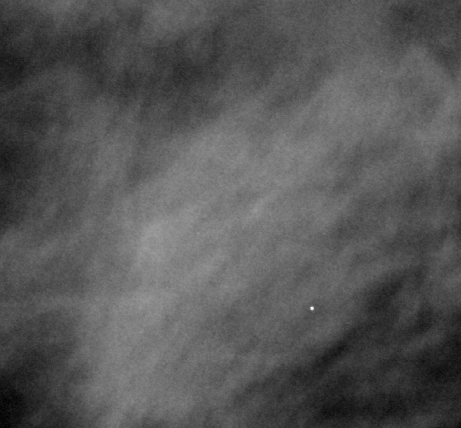
Region of interest cut from a scanned film mammogram (one marked finding), right breast, MLO view, BI-RADS breast density category 2 (scale 1–4).
Marked abnormality: mass, shape oval, margins obscured; BI-RADS assessment category 4; pathology (as recorded): benign.